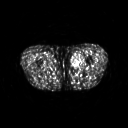
FDG PET of an extremity soft-tissue mass (from a PET/CT study), one axial slice; position 251 of 311 along the scan axis; 128 × 128 image matrix, field of view 500 × 500 mm. Patient: male, 29 years. From the clinical record (not read from this slice): histological type: mixoid liposarcoma; grade: low; site of the primary tumour: left thigh.
Outlined on this slice (expert contour drawn on MRI and transferred to this co-registered scan by the dataset authors):
- gross tumour volume (mass): bounding box (x1, y1, x2, y2) in pixels: (70, 54, 83, 68)